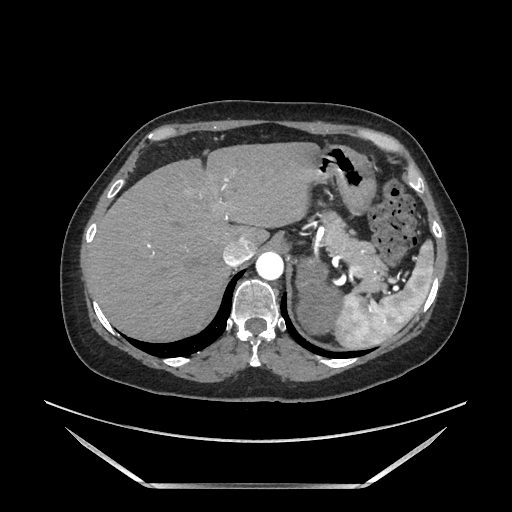
Contrast-enhanced abdominal CT, one axial slice. Position 143 of 205 along the scan axis. Soft-tissue window (W 400 / L 40 HU). 1.25 mm slice thickness. 512 × 512 image matrix, field of view 440 × 440 mm. Female patient. From the clinical record (not read from this slice): diagnosis: adrenocortical carcinoma; tumour side: left adrenal; tumour size at pathology: 12.5 cm; Ki-67 index: 39 %; stage (as recorded): 3.
Outlined on this slice (semi-automatically segmented with operator editing):
- mass: bounding box [x1, y1, x2, y2] px = [298, 259, 341, 333]